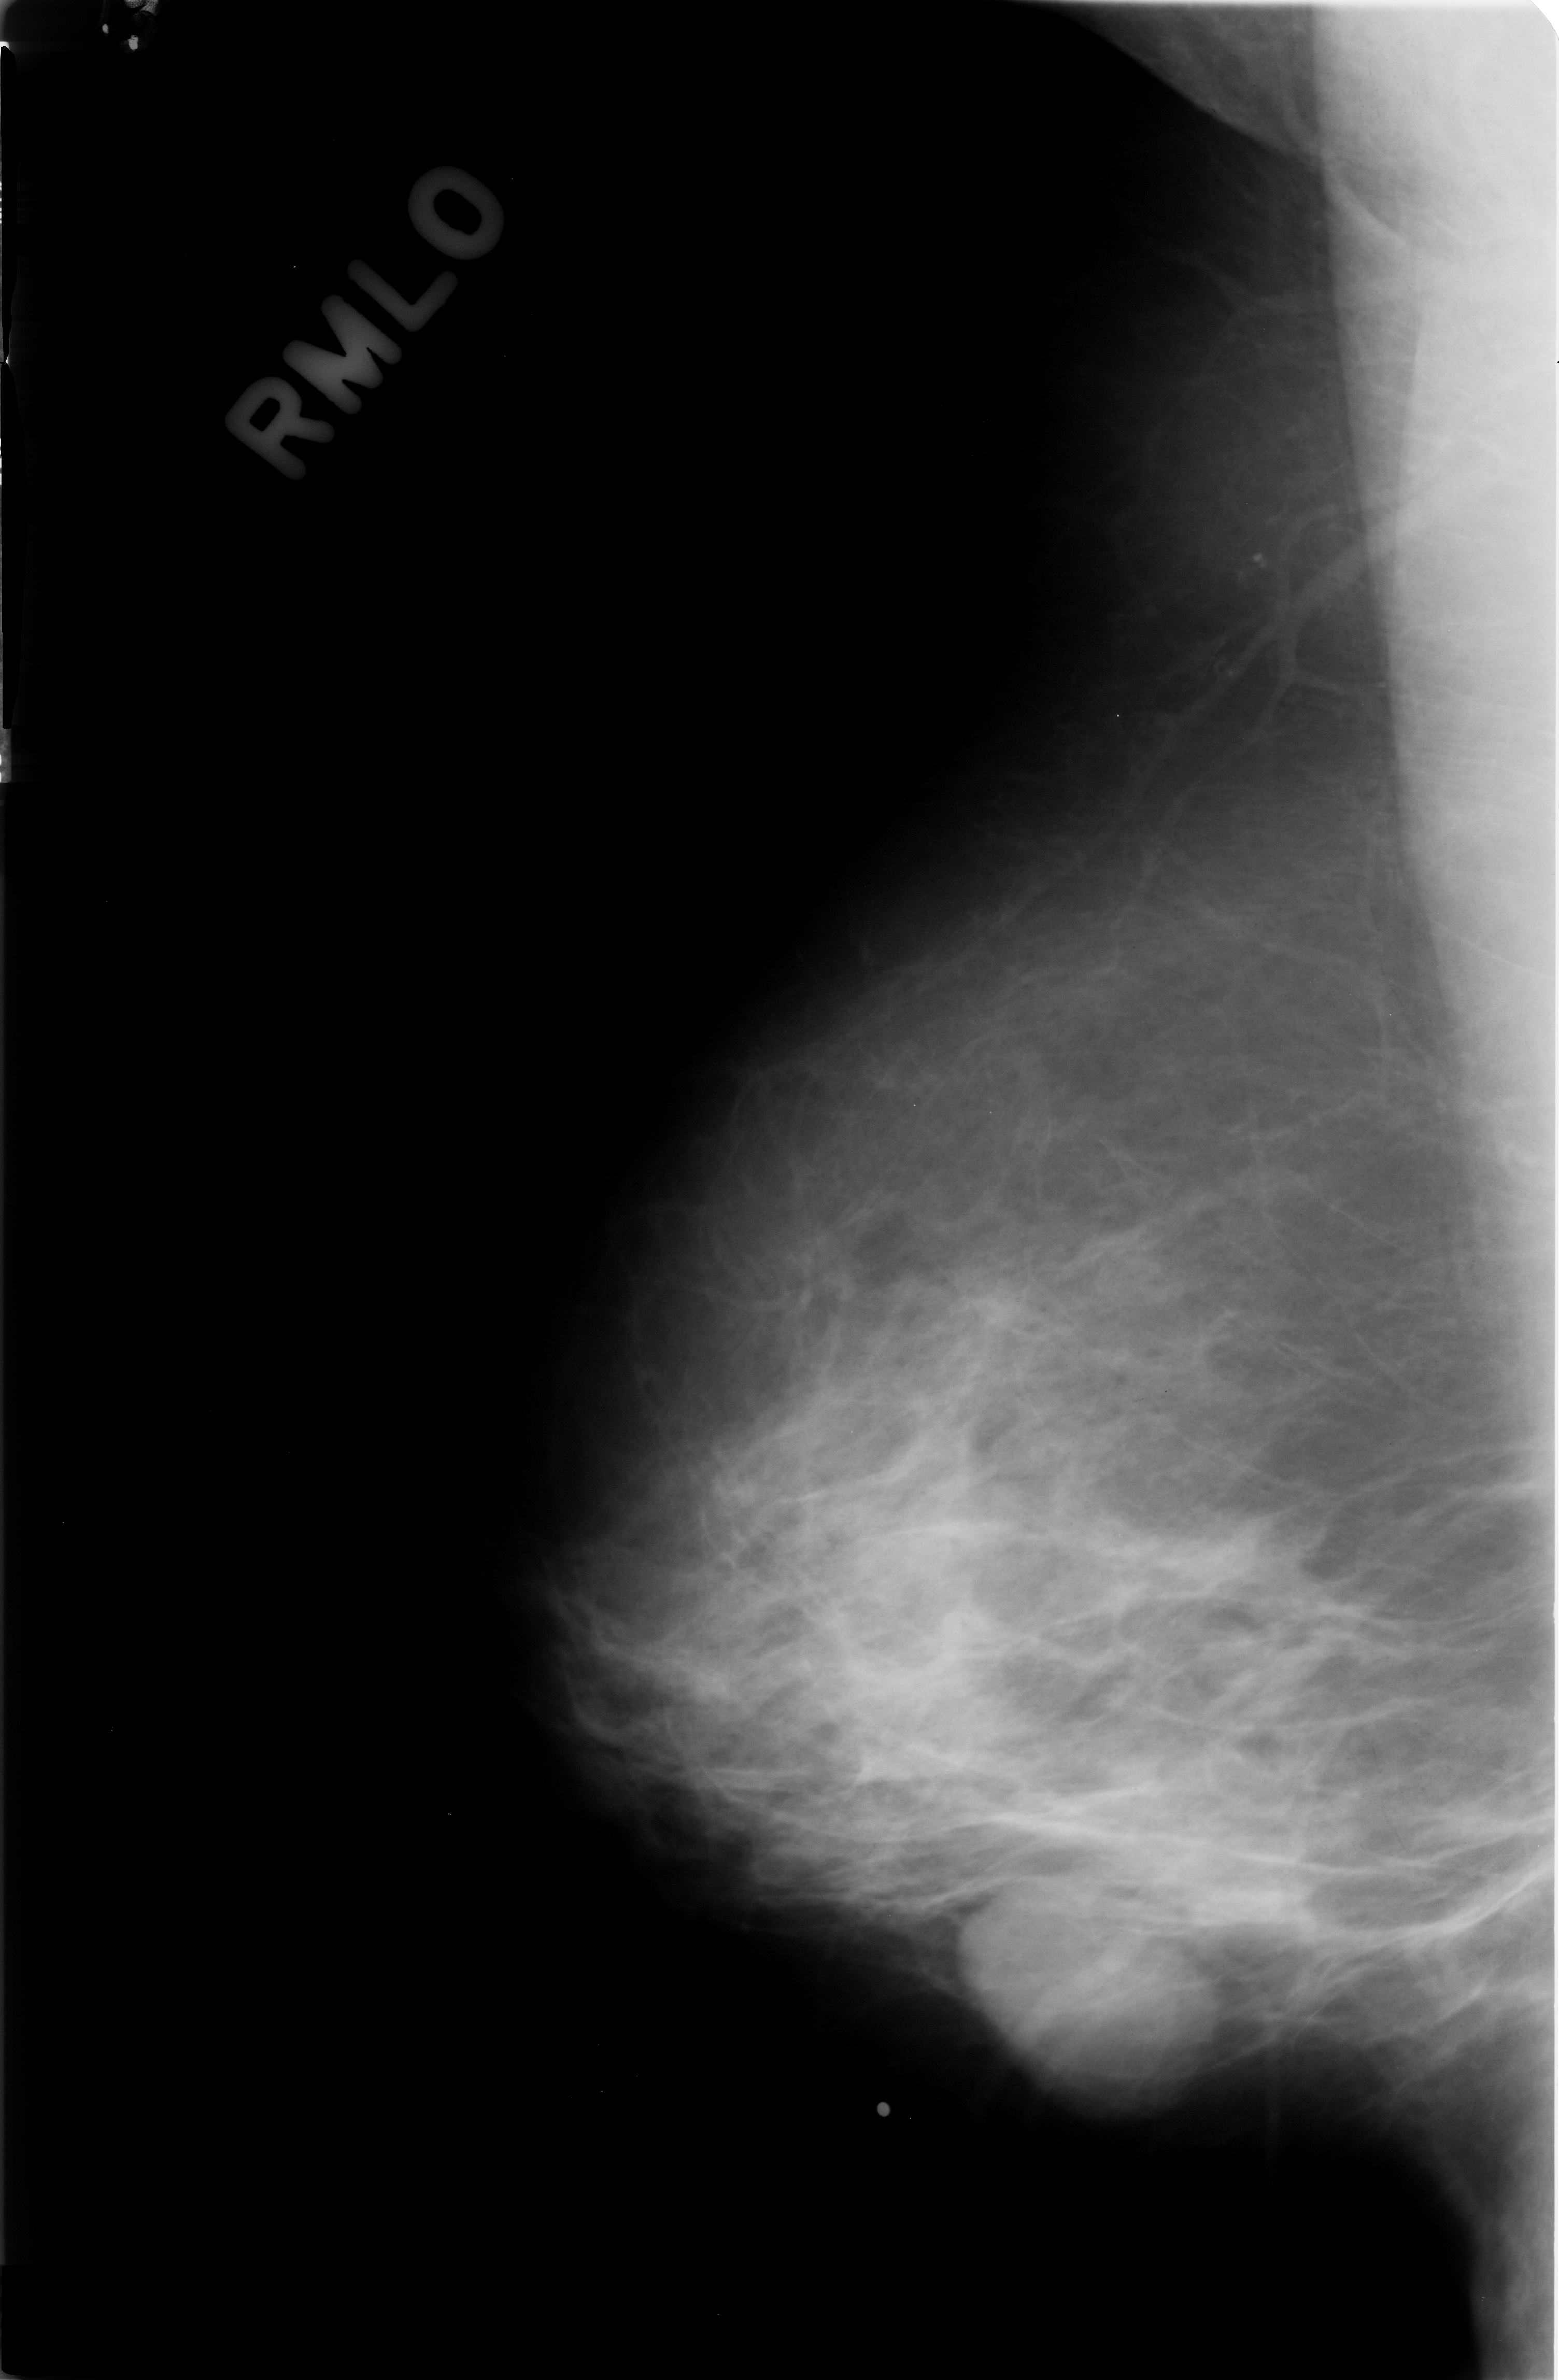
Mammogram (digitized film); right breast; MLO view; BI-RADS breast density category 2 (scale 1–4); 1559 × 2380 image matrix.
Expert-marked regions of interest on this image (one box per marked abnormality):
- mass, shape oval, margins circumscribed; BI-RADS assessment category 3; pathology result (as recorded, not read from the image): benign: box from (x=930, y=1908) to (x=1236, y=2128) px